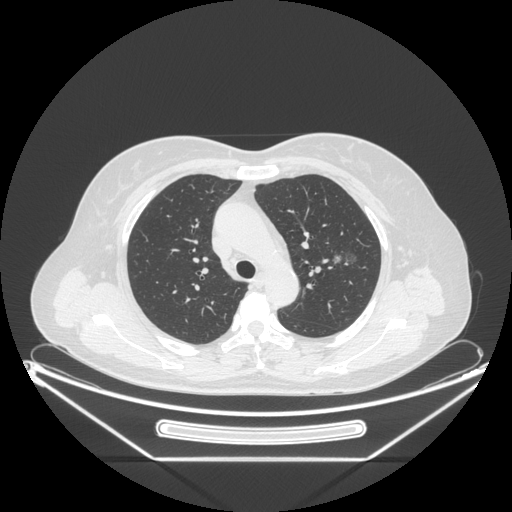
Chest CT, one axial slice. Position 152 of 226 along the scan axis. Lung window (W 1500 / L -600 HU). 512 × 512 image matrix, field of view 447 × 447 mm. Patient: female, 54 years. From the clinical record (not read from this slice): clinical TNM (as recorded): T1c N0 M0; histopathological grade: G1.
Outlined on this slice (bounding box drawn by a radiologist):
- lung tumour (recorded histology: adenocarcinoma): box from (x=319, y=243) to (x=359, y=277) px